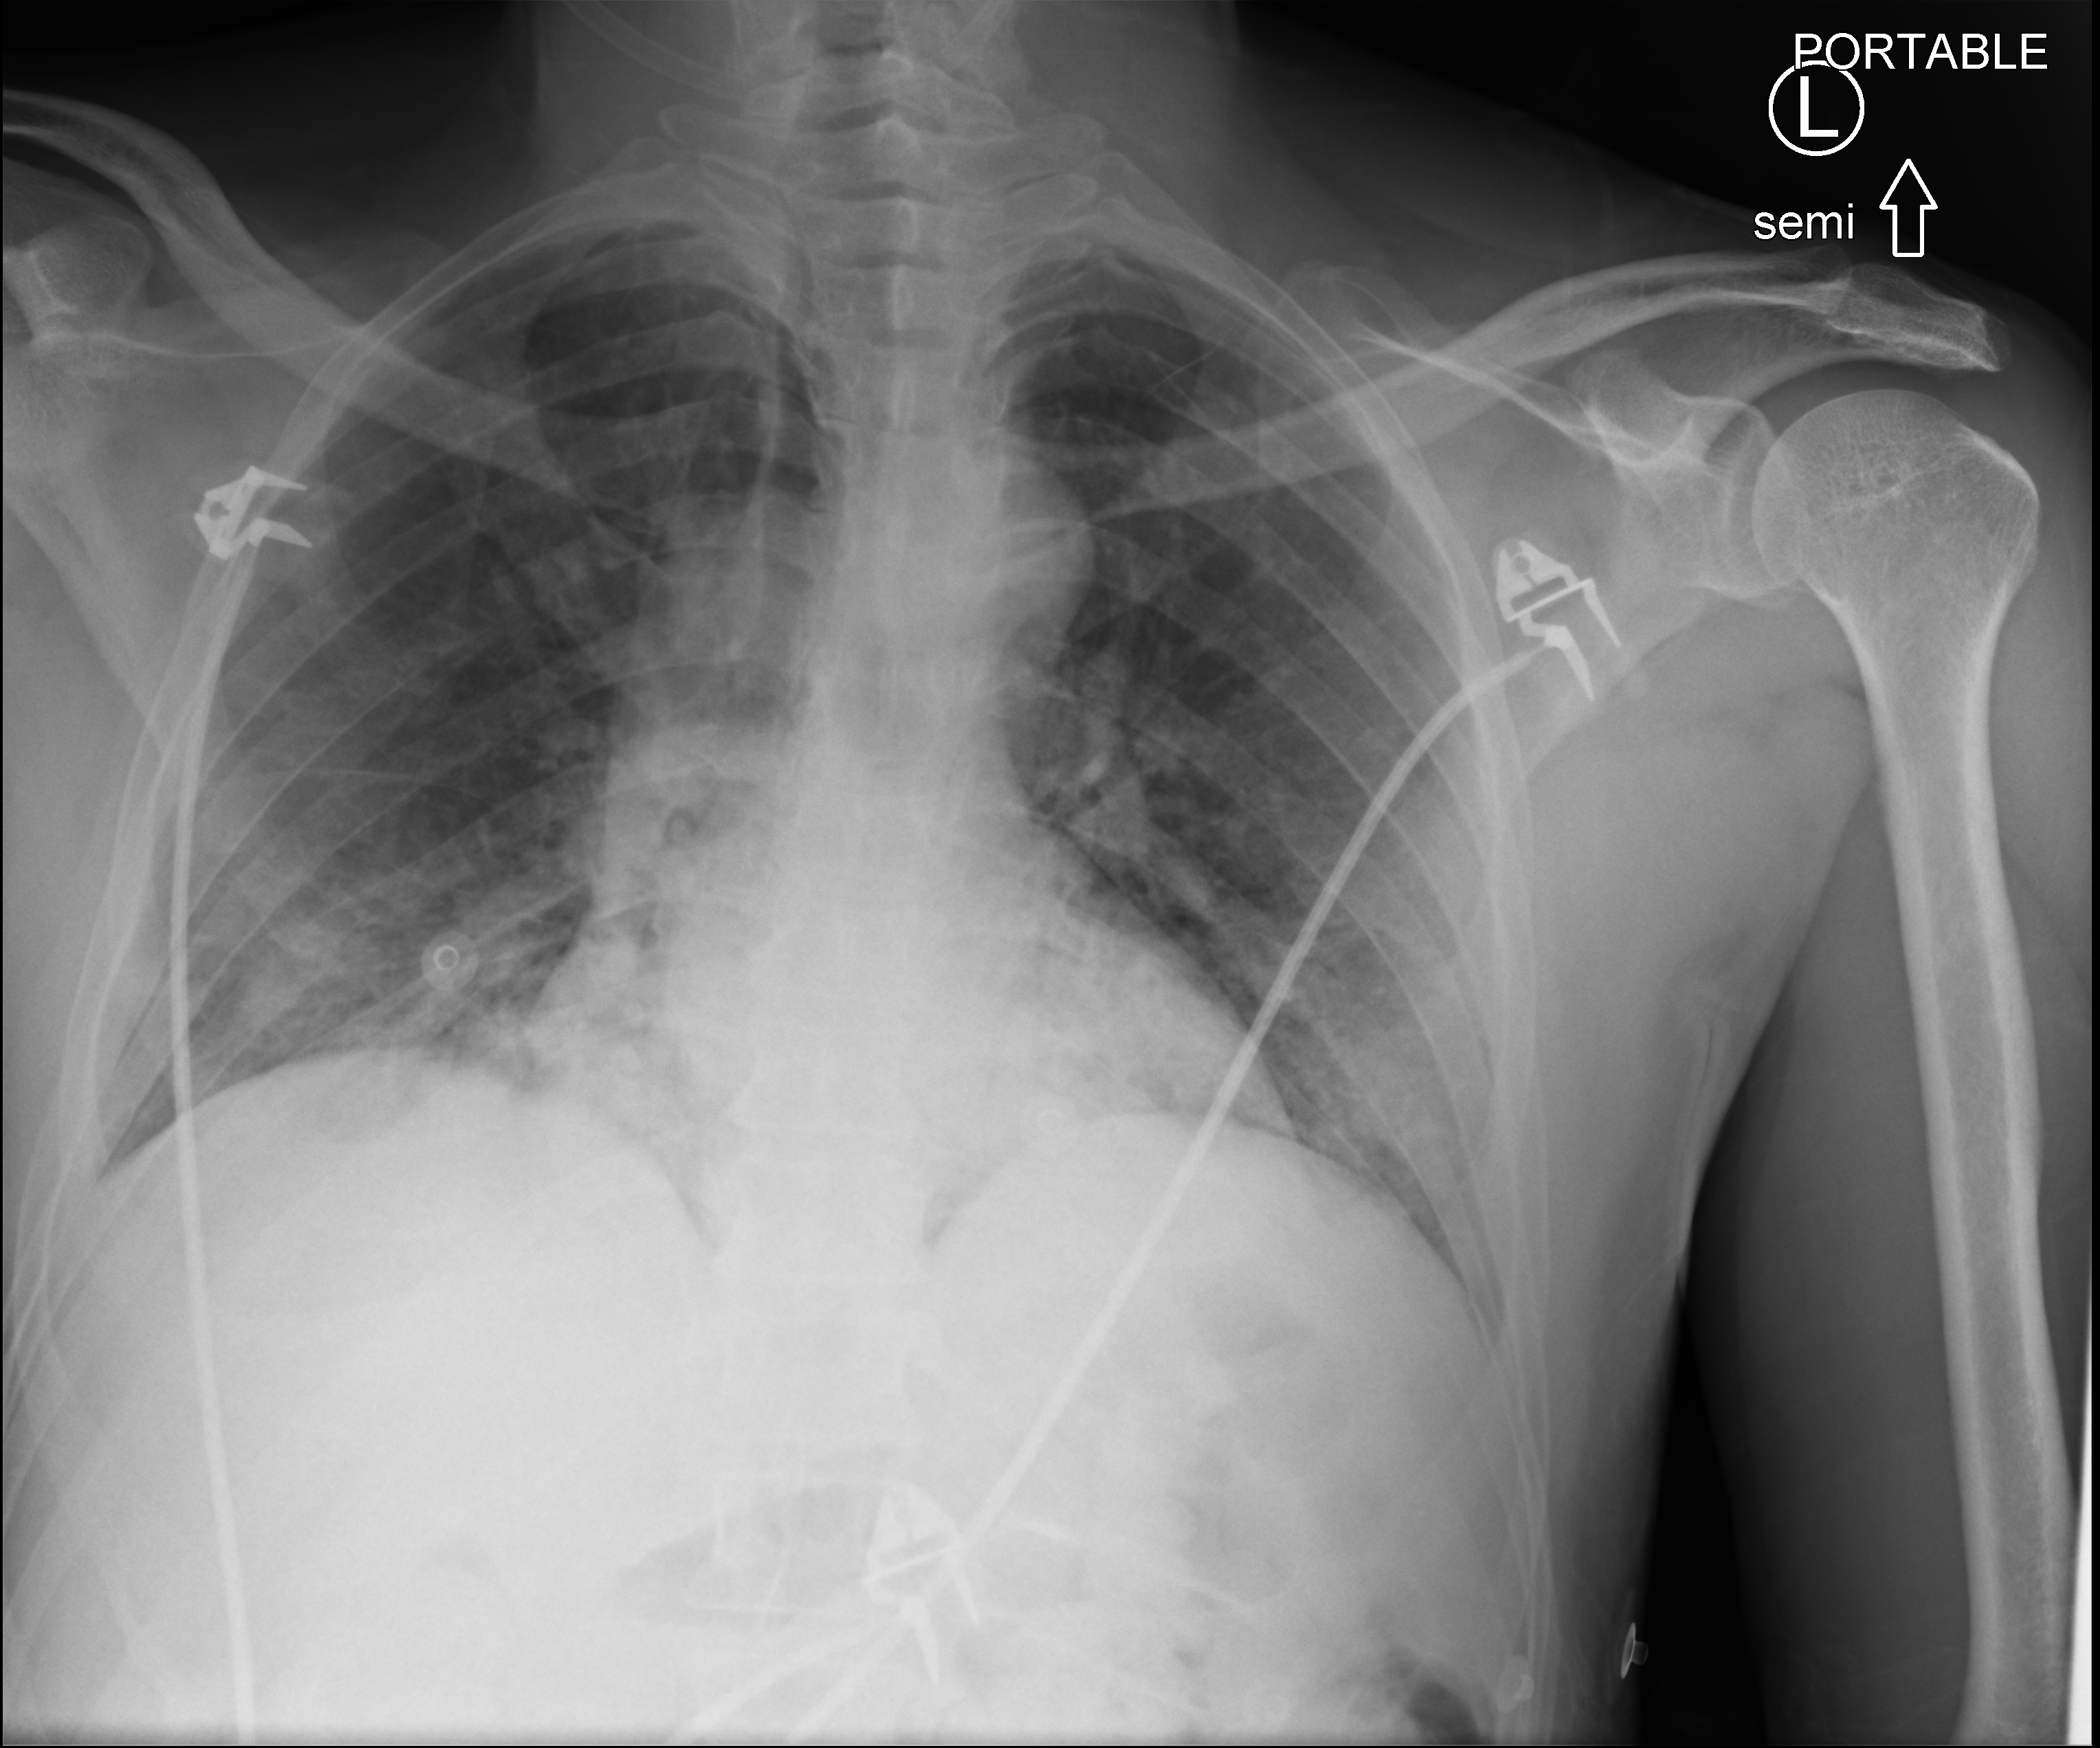
Portable chest radiograph, anteroposterior (AP) projection. Male patient hospitalised with COVID-19, age 18–59 years.
From the hospital-stay record, not from the radiograph (when in the stay this image was taken is not recorded): admitted to intensive care during this hospital stay: yes.